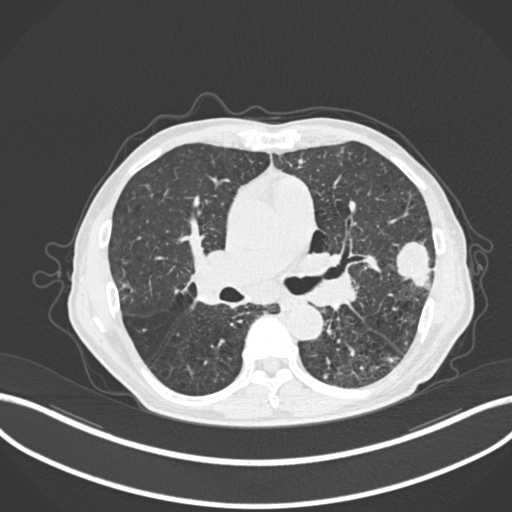
Chest CT, one axial slice; position 135 of 287 along the scan axis; reconstruction kernel B30f; 120 kVp; lung window (W 1500 / L -600 HU); 512 × 512 image matrix, field of view 400 × 400 mm. Male patient, age 74 years. Case-level facts recorded for this patient, not image findings: clinical TNM (as recorded): T2a N1 M0.
Outlined on this slice (rectangle marked by the reading radiologist):
- lung tumour (recorded histology: adenocarcinoma): box from (x=389, y=236) to (x=436, y=298) px